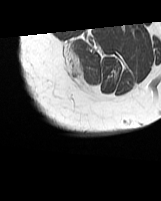
MRI of an extremity soft-tissue mass, one axial slice; position 8 of 70 along the scan axis; MR volume resampled by the dataset authors to the PET/CT grid (not the native acquisition matrix); 3.27 mm slice thickness; 161 × 201 image matrix, field of view 157 × 196 mm. Female patient. Case-level facts recorded for this patient, not image findings: histological type: synovial sarcoma; grade: intermediate; site of the primary tumour: right buttock.
Outlined on this slice (expert contour drawn on MRI and transferred to this co-registered scan by the dataset authors):
- gross tumour volume including surrounding oedema: box from (x=63, y=43) to (x=82, y=82) px